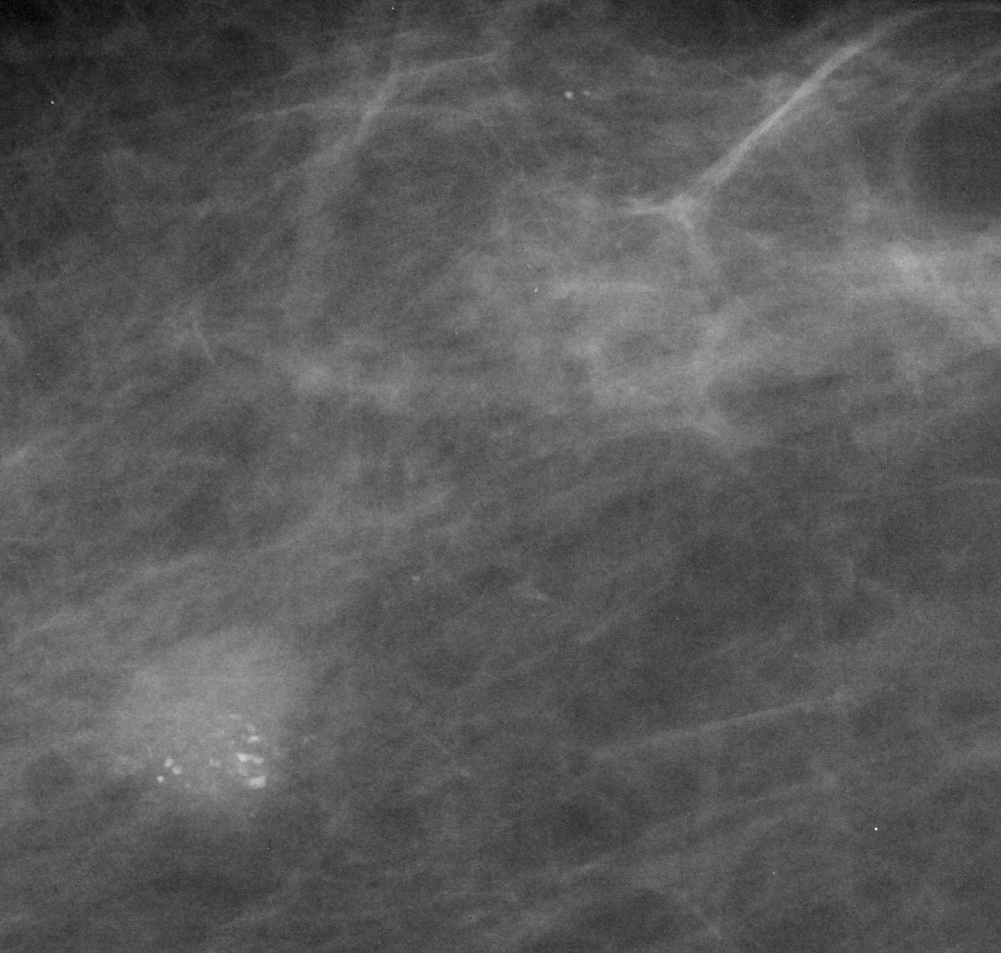
Region of interest cut from a scanned film mammogram (one marked finding), left breast, CC view.
Marked abnormality: calcifications, morphology pleomorphic, distribution clustered; BI-RADS assessment category 4; pathology (as recorded): malignant.